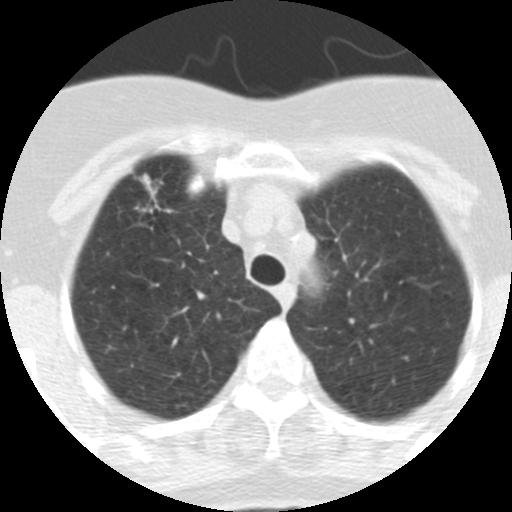
Chest CT (low-dose screening protocol), one axial image, baseline annual screen, lung window (W 1500 / L -600 HU), 2.5 mm slice thickness, 120 kVp, slice 62 of 313 in the series. Female participant, aged 62 years at enrolment.
Expert reader's lesion annotation, bounding box (x1, y1, x2, y2) in pixels: (116, 169, 189, 237). Screening reader's record for this exam (one nodule recorded; not confirmed to be the boxed lesion): non-calcified nodule or mass ≥4 mm, right upper lobe, 9 × 7 mm, spiculated (stellate) margins, soft tissue attenuation. Official screen result: positive, change unspecified: nodule(s) >= 4 mm or enlarging nodule(s), mass(es), or other non-specific abnormalities suspicious for lung cancer. Lung cancer was diagnosed 126 days after this screen: adenocarcinoma, NOS, right upper lobe, moderately differentiated (G2), stage IA (AJCC 6th edition), 18 mm at pathology.